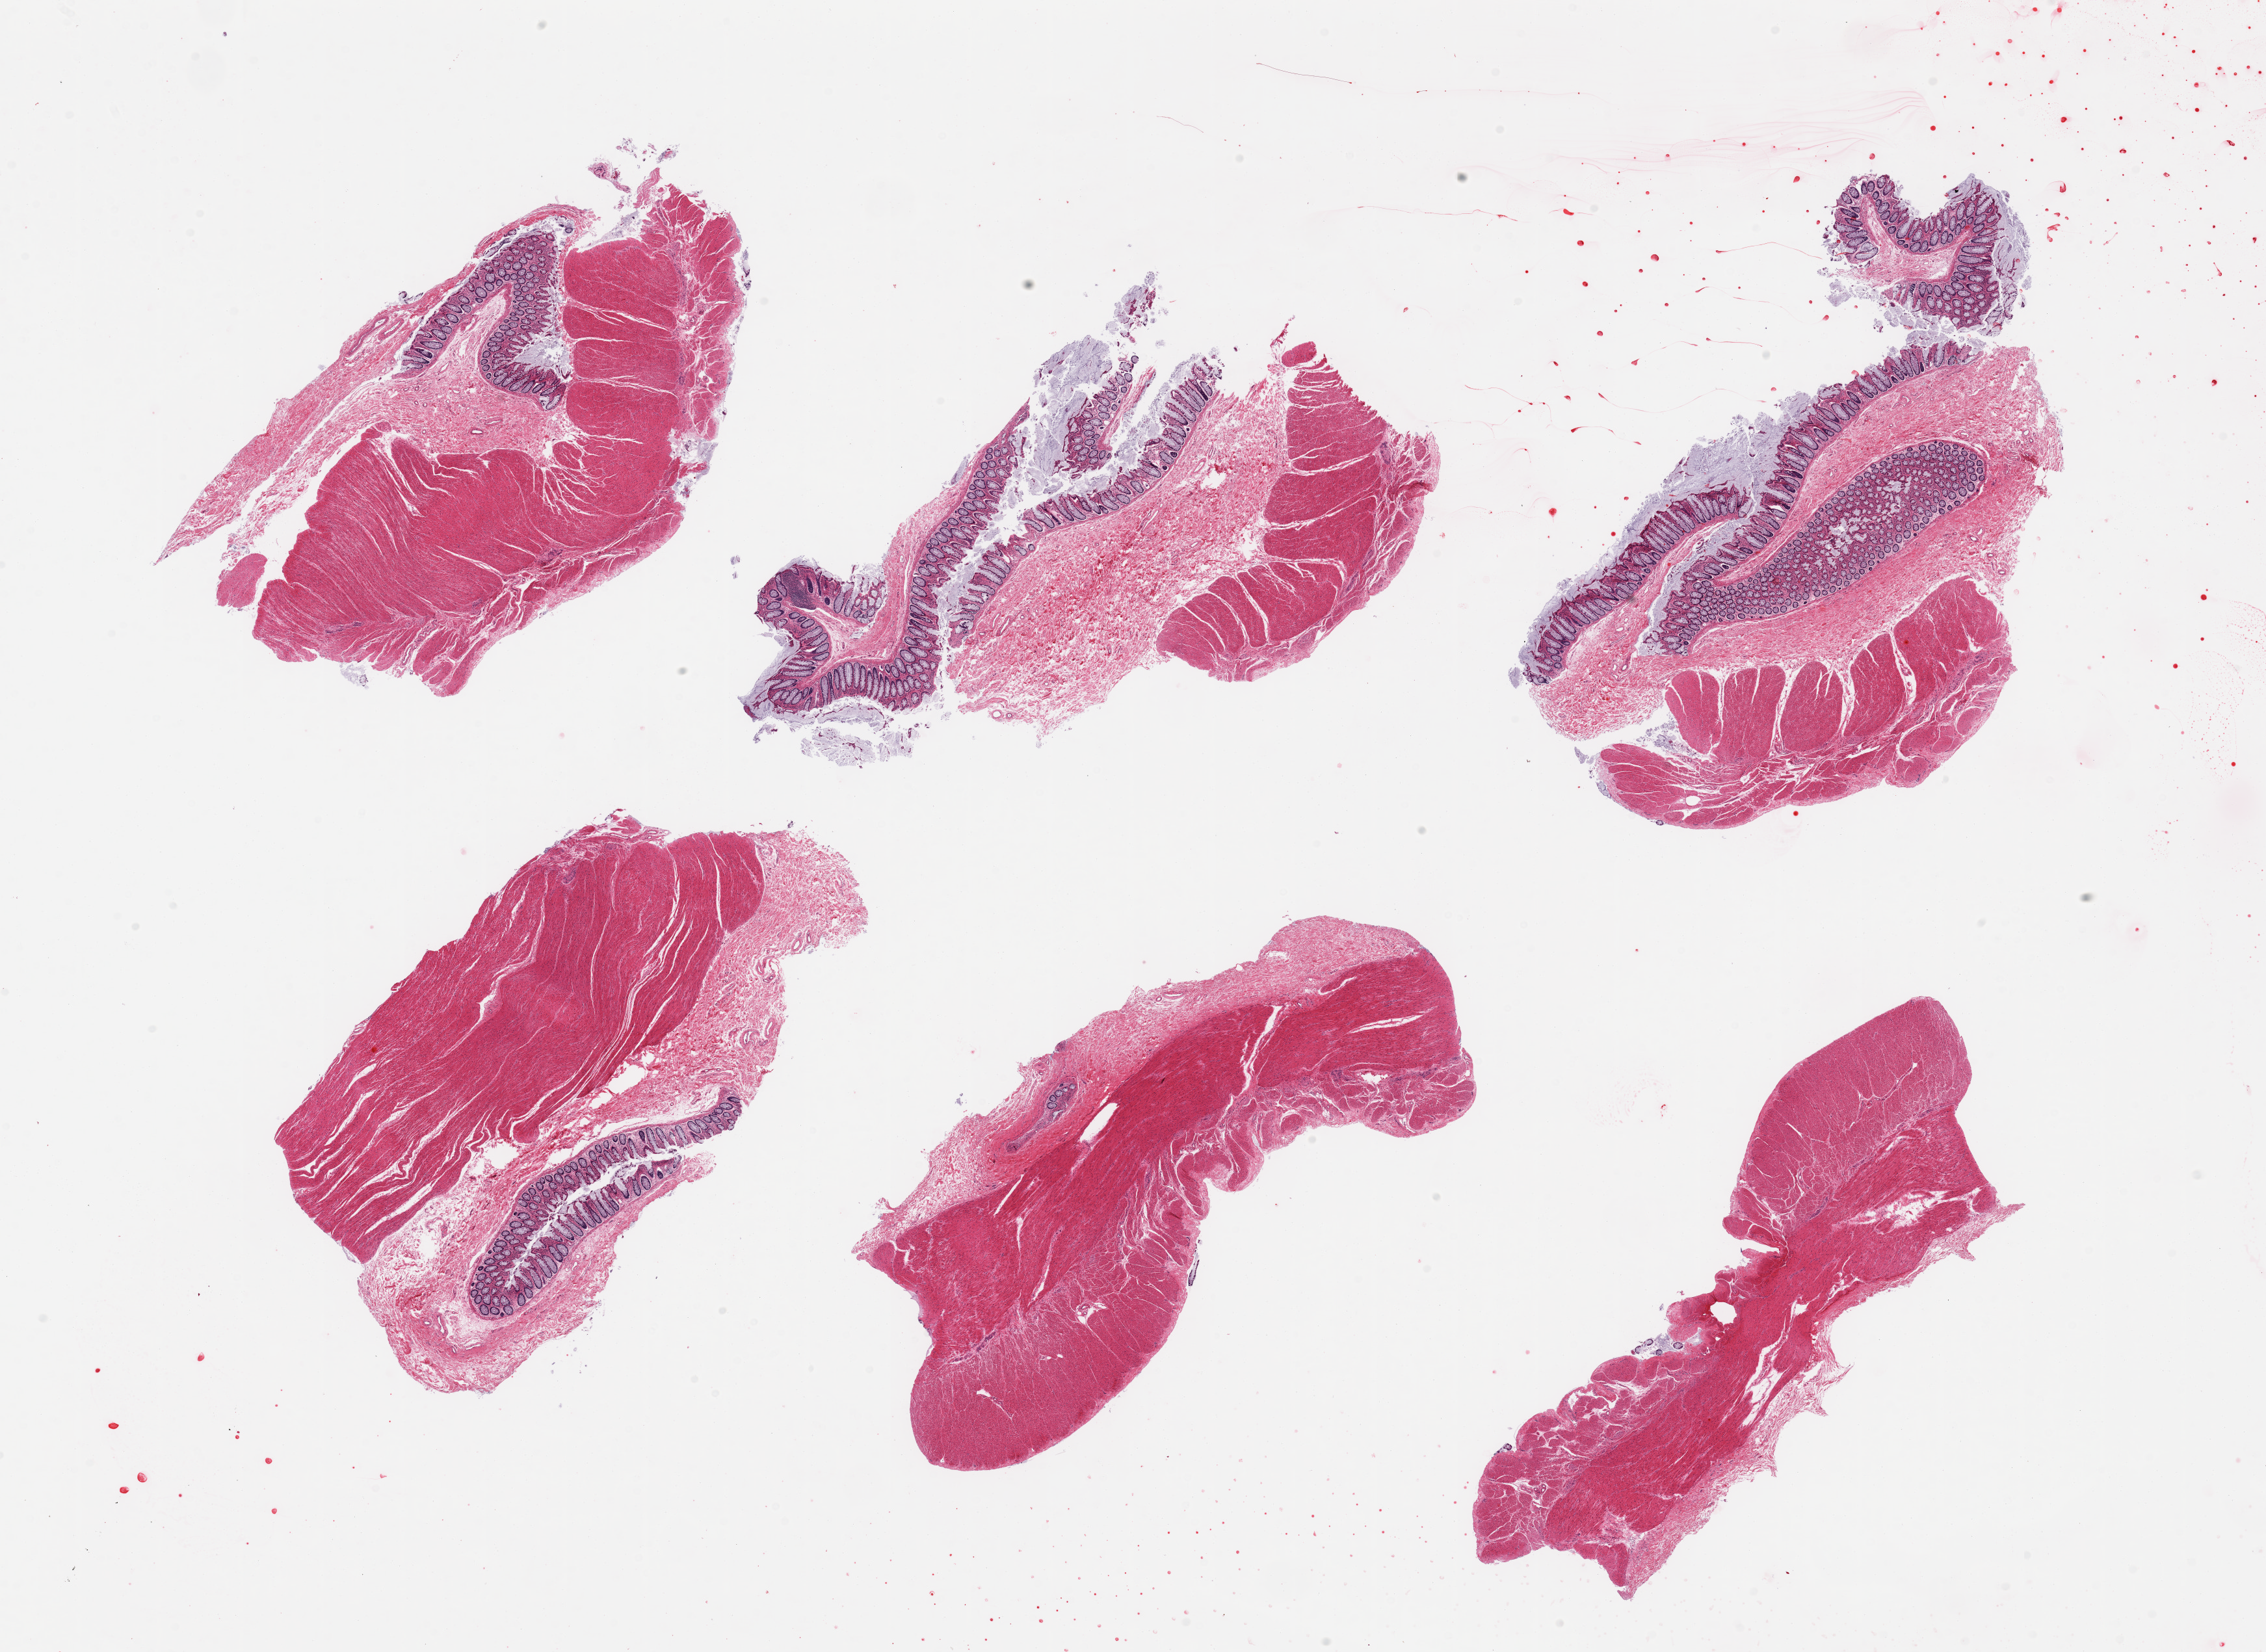
Whole-slide image, haematoxylin and eosin stain, brightfield — a low-resolution overview of the entire scanned area, about 27.6 x 20.1 mm; PAXgene-fixed, paraffin-embedded tissue; section of sigmoid colon (target tissue); tissue donor sample.
Review note (as recorded): 6 pieces; 3 pieces contain mildly to moderately autolyzed non target mucosa; target muscularis present.